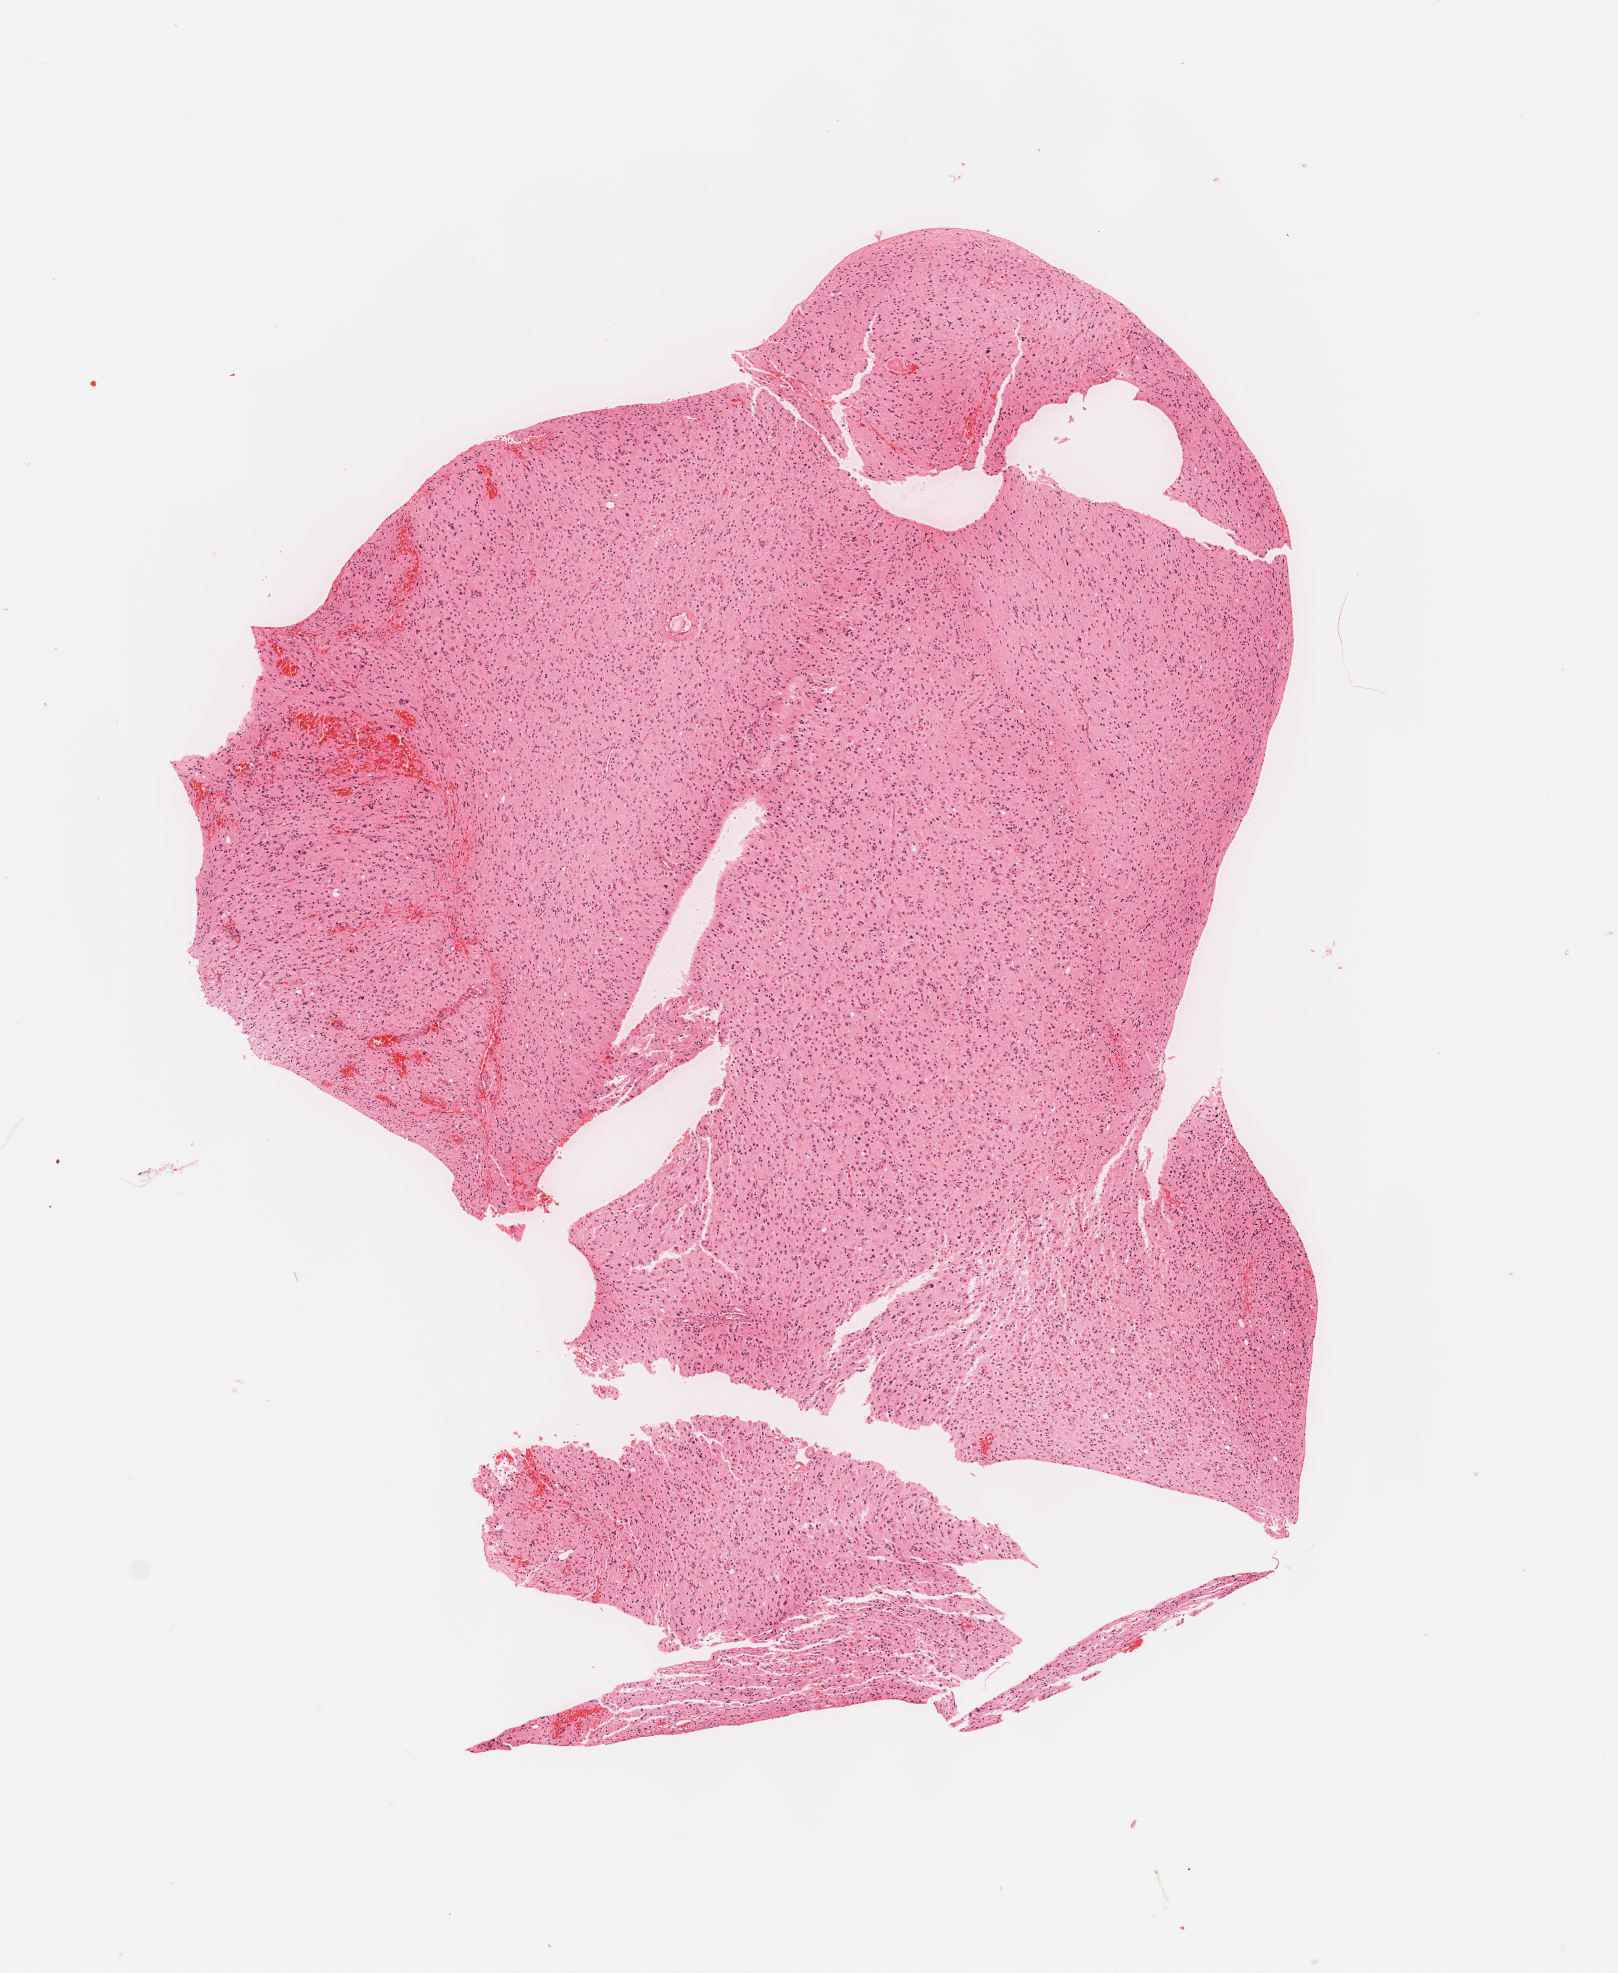
Digitized H&E-stained tissue section (whole slide) — shown as a low-resolution overview of the whole scanned area (about 6.5 x 8.0 mm). Formalin-fixed paraffin-embedded (FFPE) diagnostic section. Sample: primary tumour, brain. Male, age 38 years at initial diagnosis. Histologic grade: G2 (moderately differentiated).
- histologic diagnosis: Astrocytoma, NOS (cerebrum)